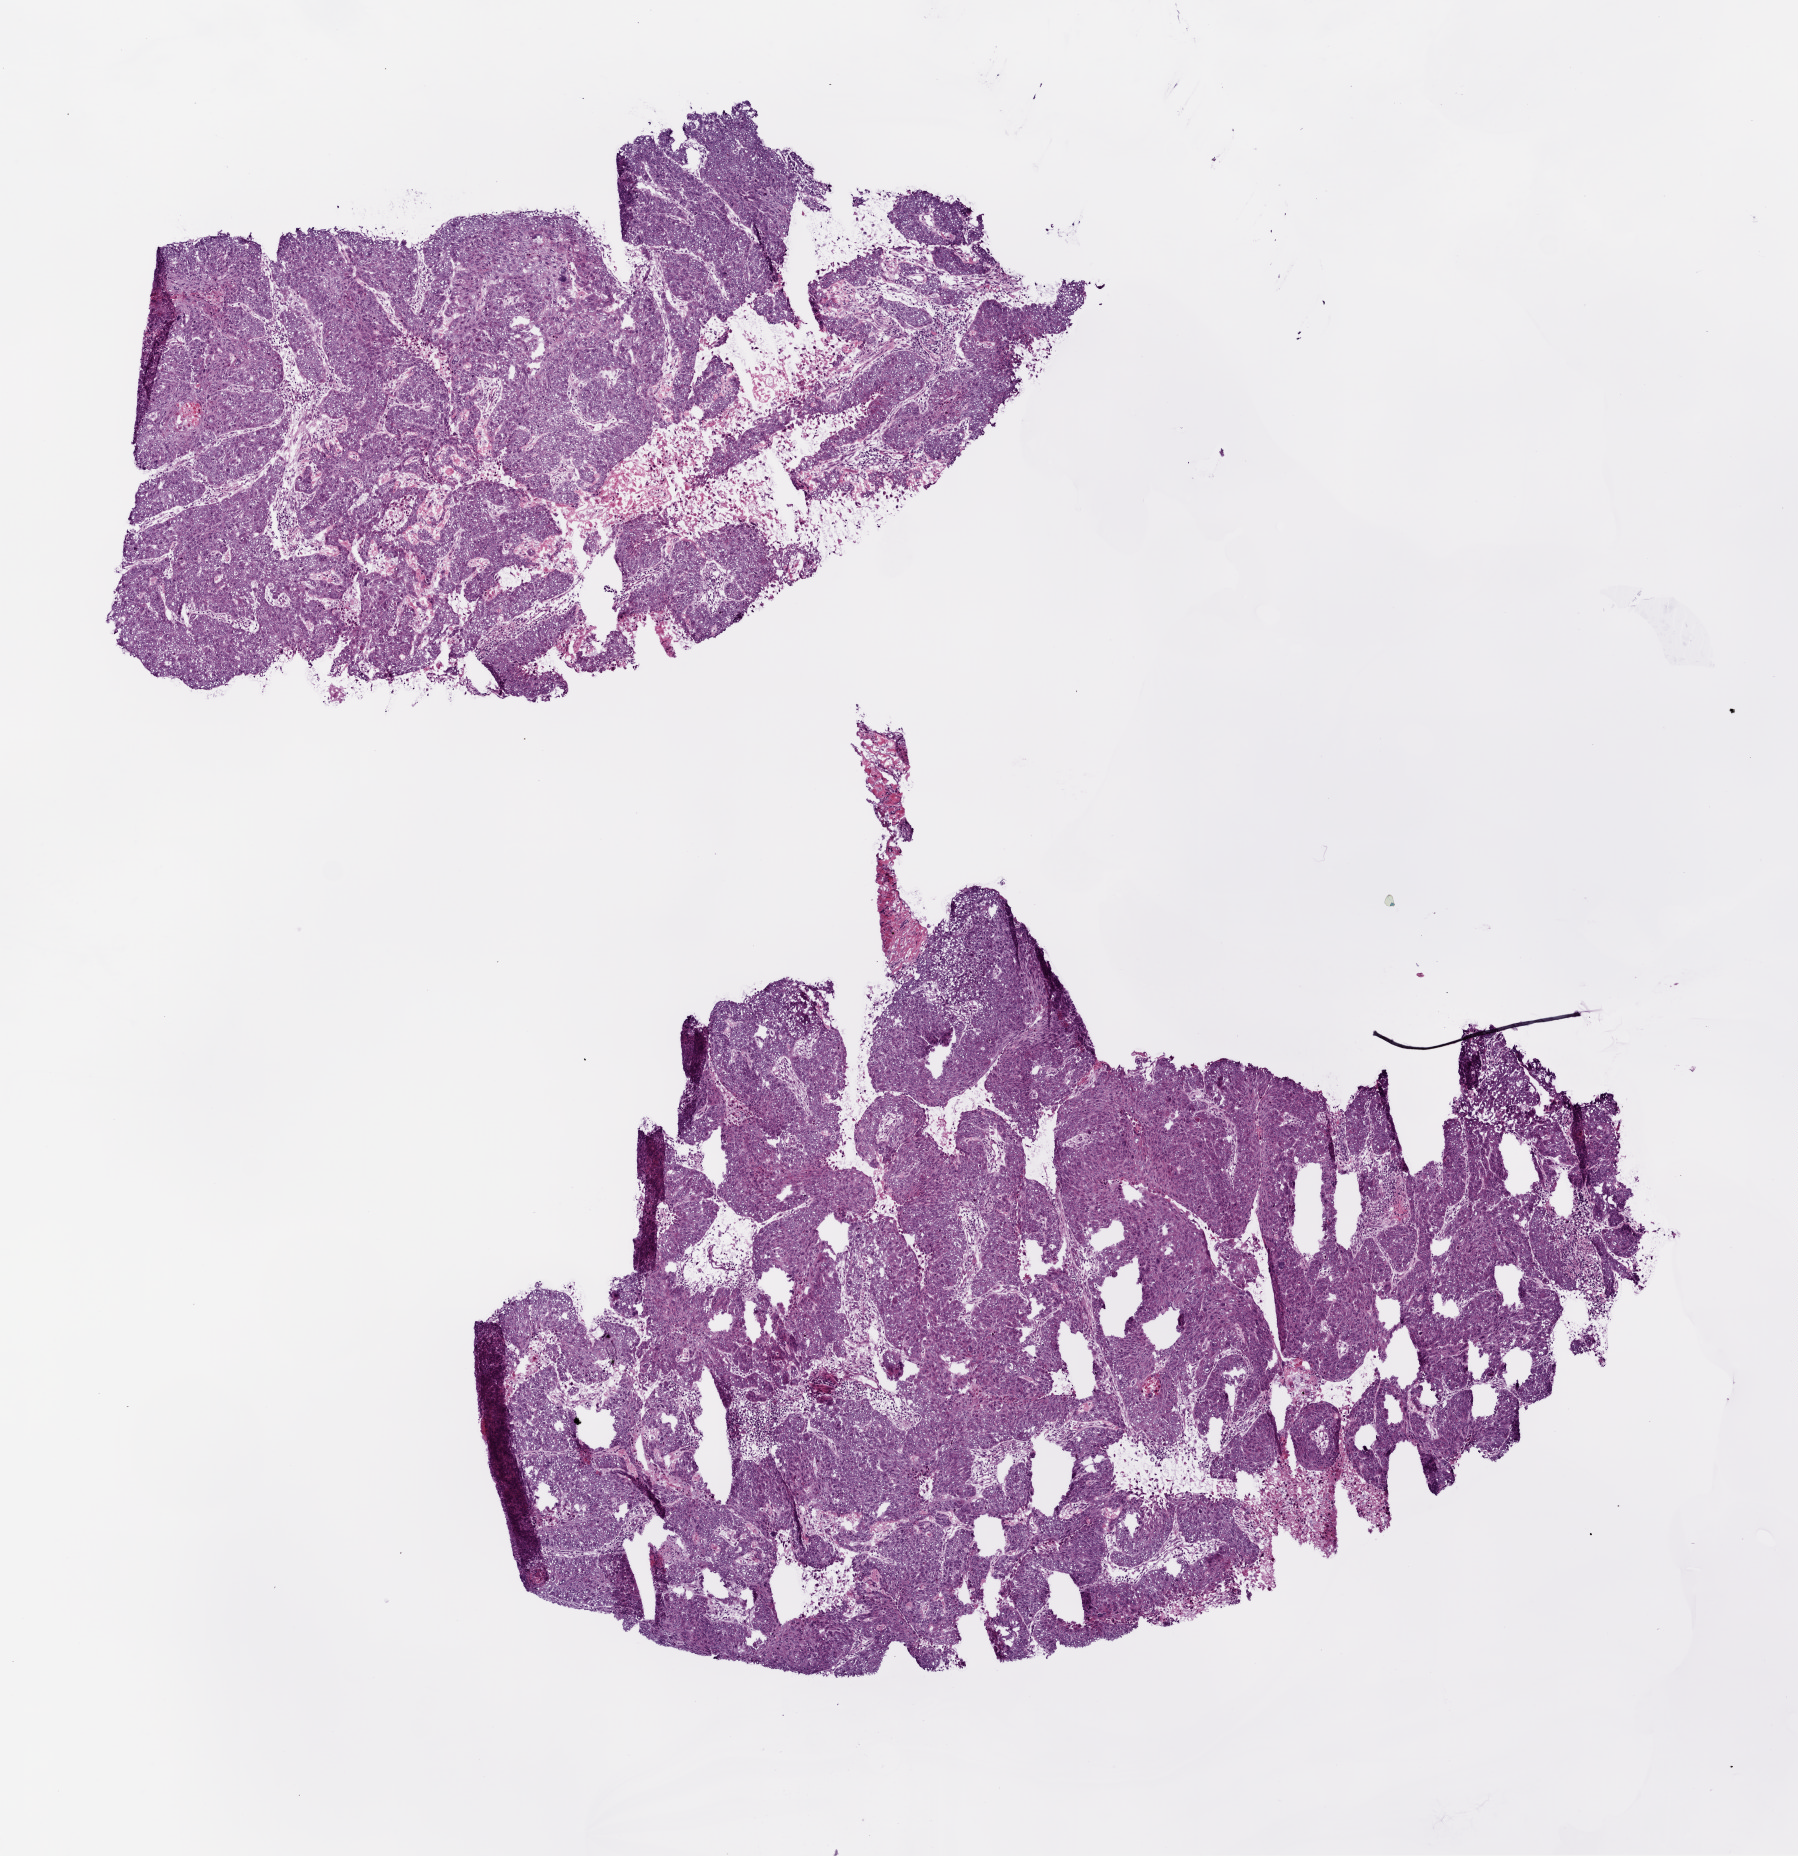
Digitized Hematoxylin and eosin (H&E) stained tissue section (whole slide) — a low-resolution overview of the entire scanned area, about 7.3 x 7.5 mm (acquisition: 20x scan). Frozen section from the top of the tissue portion. Sample: primary tumour, lung. Patient: male, age at initial diagnosis 57 years. Pathologist review of this section (percent, as recorded): tumour cells 90%, tumour nuclei 85%, normal cells 0%, stromal cells 5%, necrosis 5%.
- laterality: left
- AJCC pathologic stage: IIB
- pathologic diagnosis: Squamous cell carcinoma, NOS (upper lobe, lung)